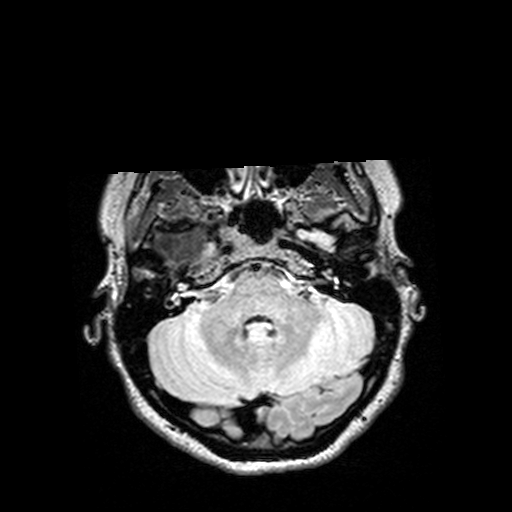
Brain MRI from a brain-tumour surgery series, one axial slice. Position 110 of 144 along the scan axis. T2 FLAIR. 512 × 512 image matrix. Case-level facts recorded for this patient, not image findings: histopathology: Astrocytoma; WHO grade: 3; IDH mutation: yes.
Annotated regions visible in this slice (manually delineated by an expert):
- tumour: bounding box (x1, y1, x2, y2) in pixels: (135, 225, 189, 263)